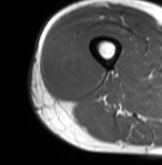
MRI of an extremity soft-tissue mass, one axial slice. Slice 26 of 61 in the series (ordered by position). MR volume resampled by the dataset authors to the PET/CT grid (not the native acquisition matrix). 3.27 mm slice thickness. 162 × 165 image matrix, field of view 158 × 161 mm. Male patient. From the clinical record (not read from this slice): histological type: poorly differentiated synovial sarcoma; grade: high; site of the primary tumour: right buttock.
Outlined on this slice (expert contour drawn on MRI and transferred to this co-registered scan by the dataset authors):
- gross tumour volume including surrounding oedema: bounding box <50,38,101,96> (left, top, right, bottom; pixels)
- gross tumour volume (mass): <52,42,90,94>